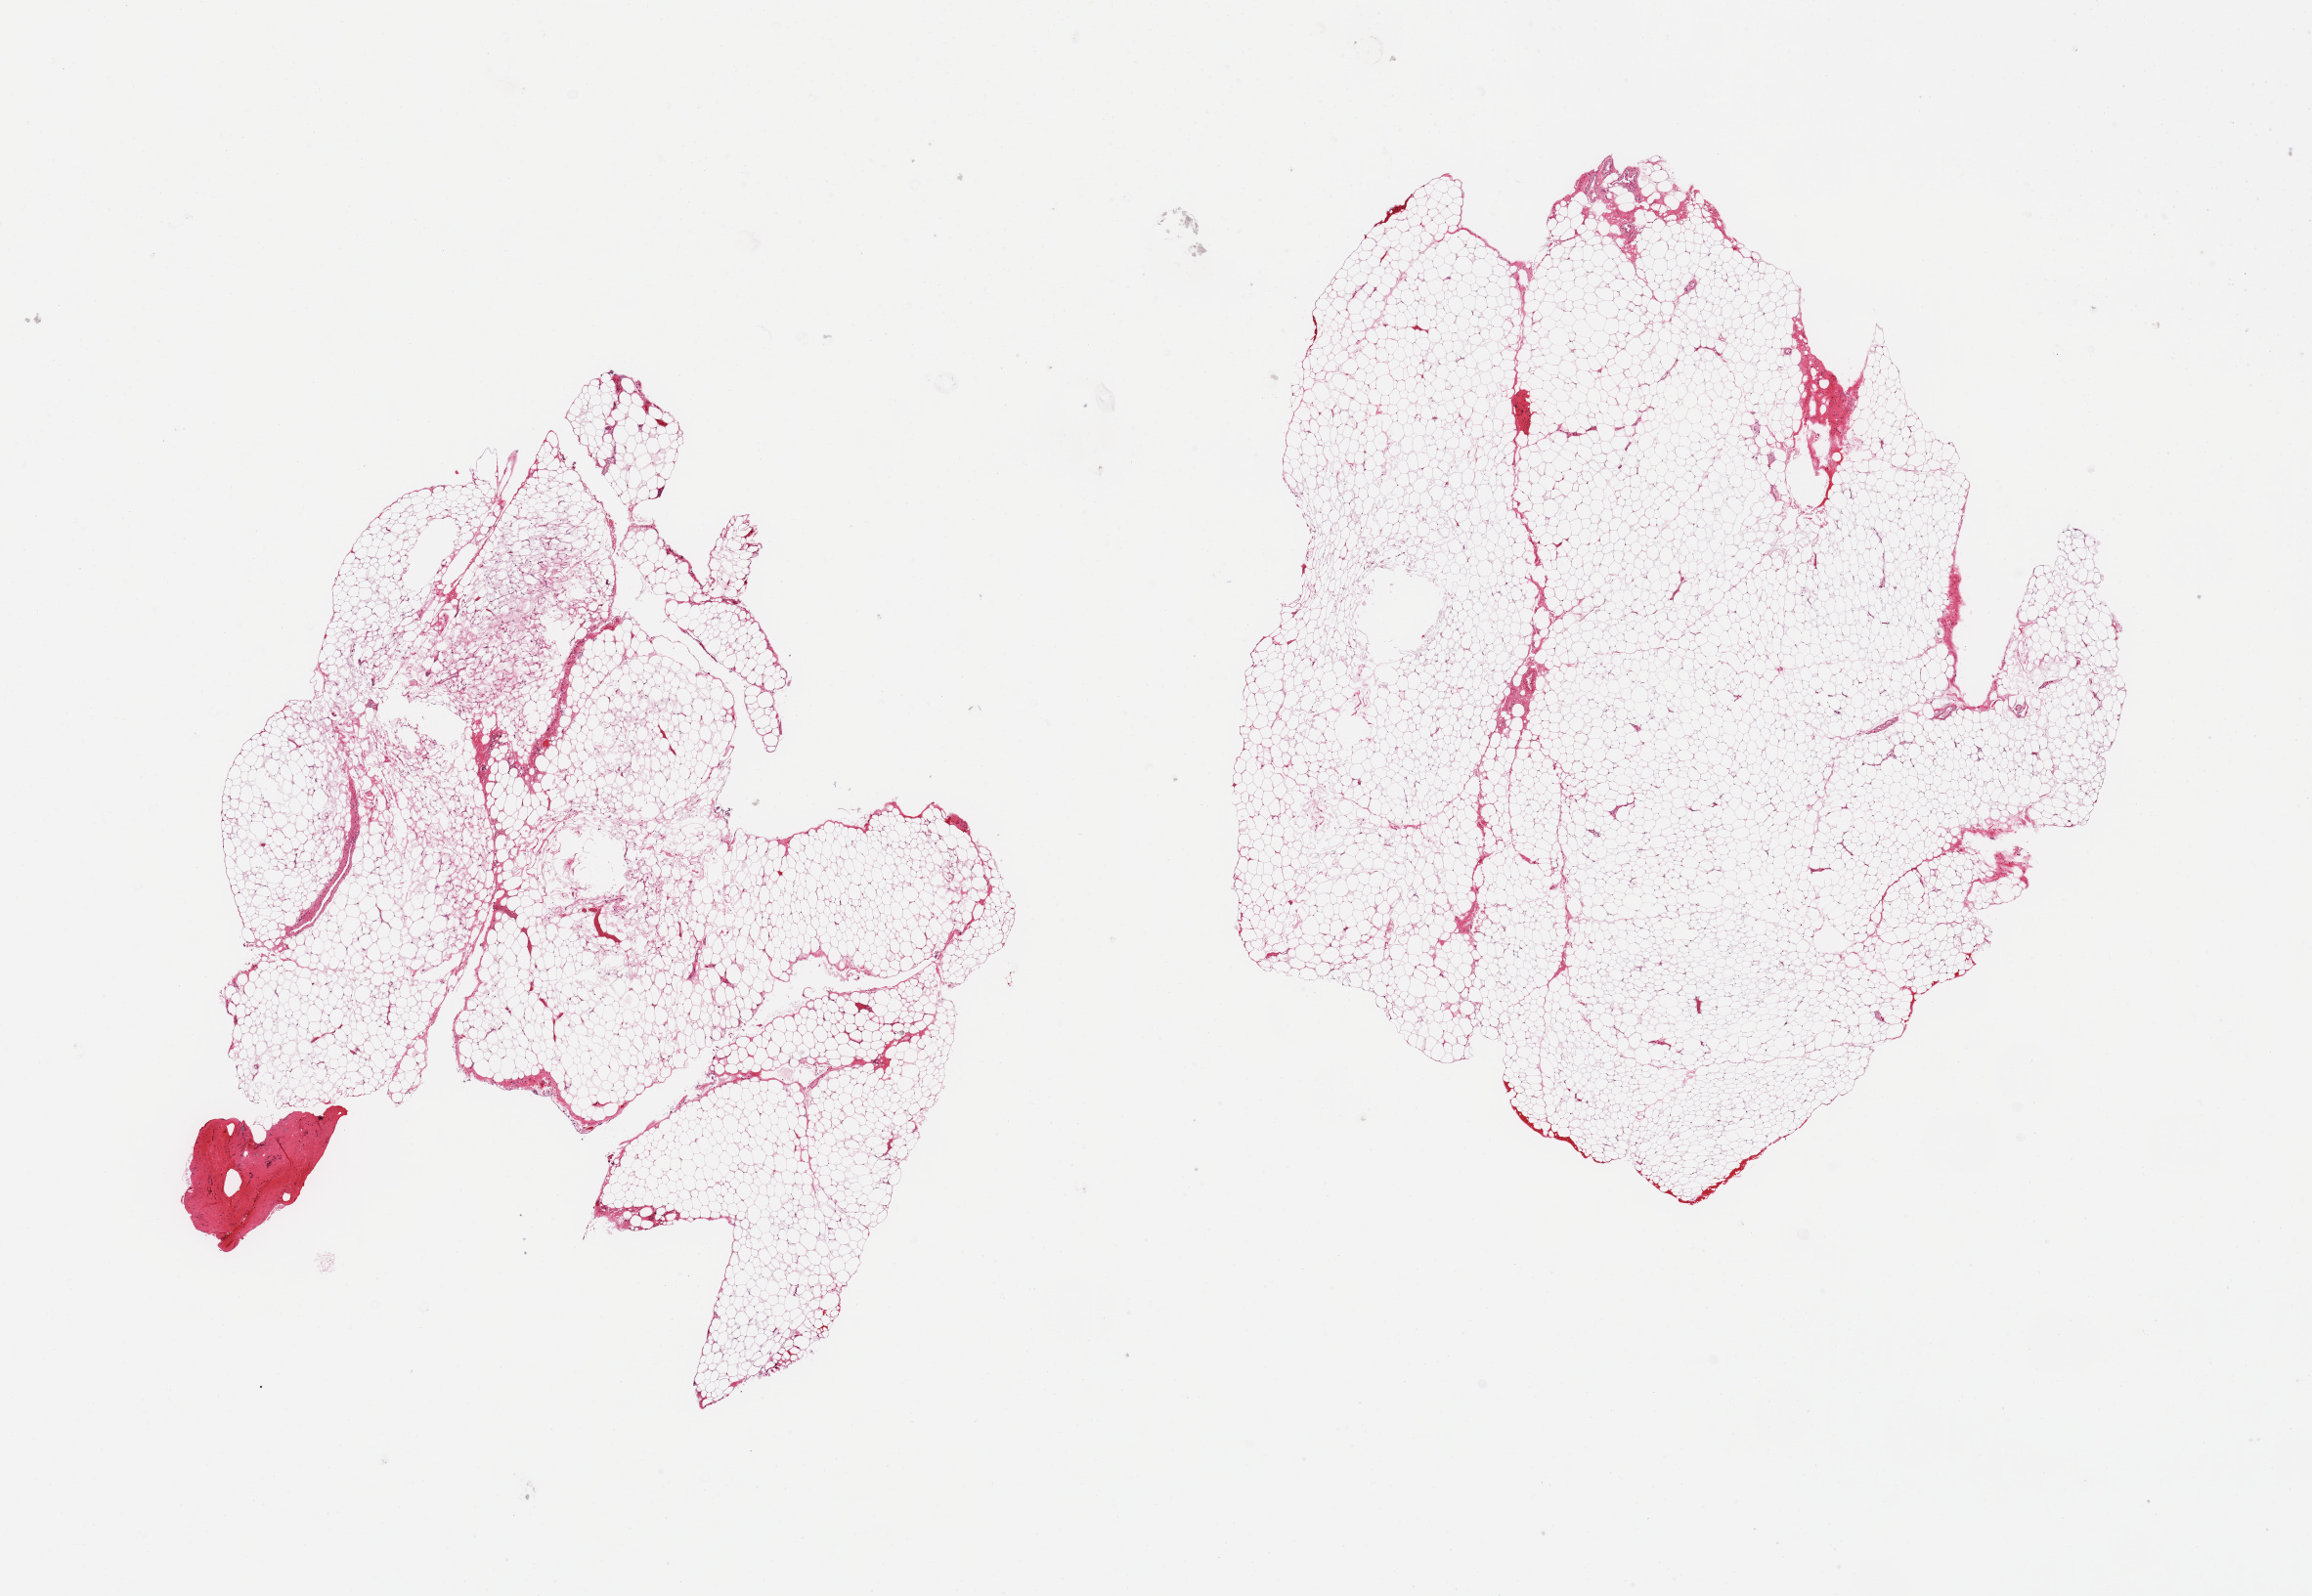
Hematoxylin and eosin (H&E) whole-slide image, brightfield, shown as a low-resolution overview of the whole scanned area (about 18.7 x 12.9 mm), PAXgene-fixed, paraffin-embedded tissue, section of omentum (target tissue), donor tissue sample. Donor: male.
Review note (as recorded): 2 pieces; mature adipose tissue, detached portion of fibrous tissue.